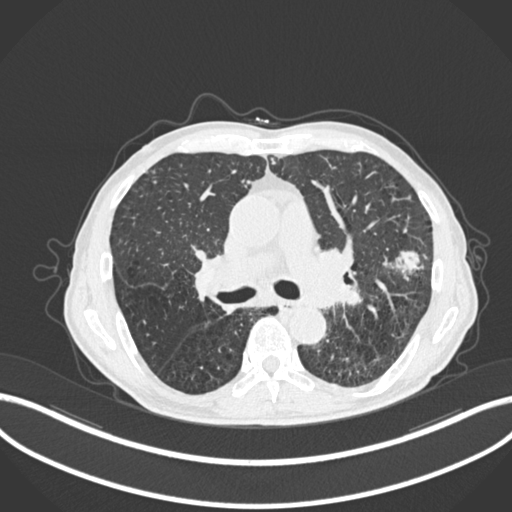
Chest CT, one axial slice; position 149 of 287 along the scan axis; reconstruction kernel B30f; lung window (W 1500 / L -600 HU); 1 mm slice thickness; 512 × 512 image matrix, field of view 400 × 400 mm. Patient: male, 74 years. Case-level facts recorded for this patient, not image findings: clinical TNM (as recorded): T2a N1 M0.
Annotated regions visible in this slice (rectangle marked by the reading radiologist):
- lung tumour (recorded histology: adenocarcinoma): box from (x=393, y=247) to (x=423, y=282) px